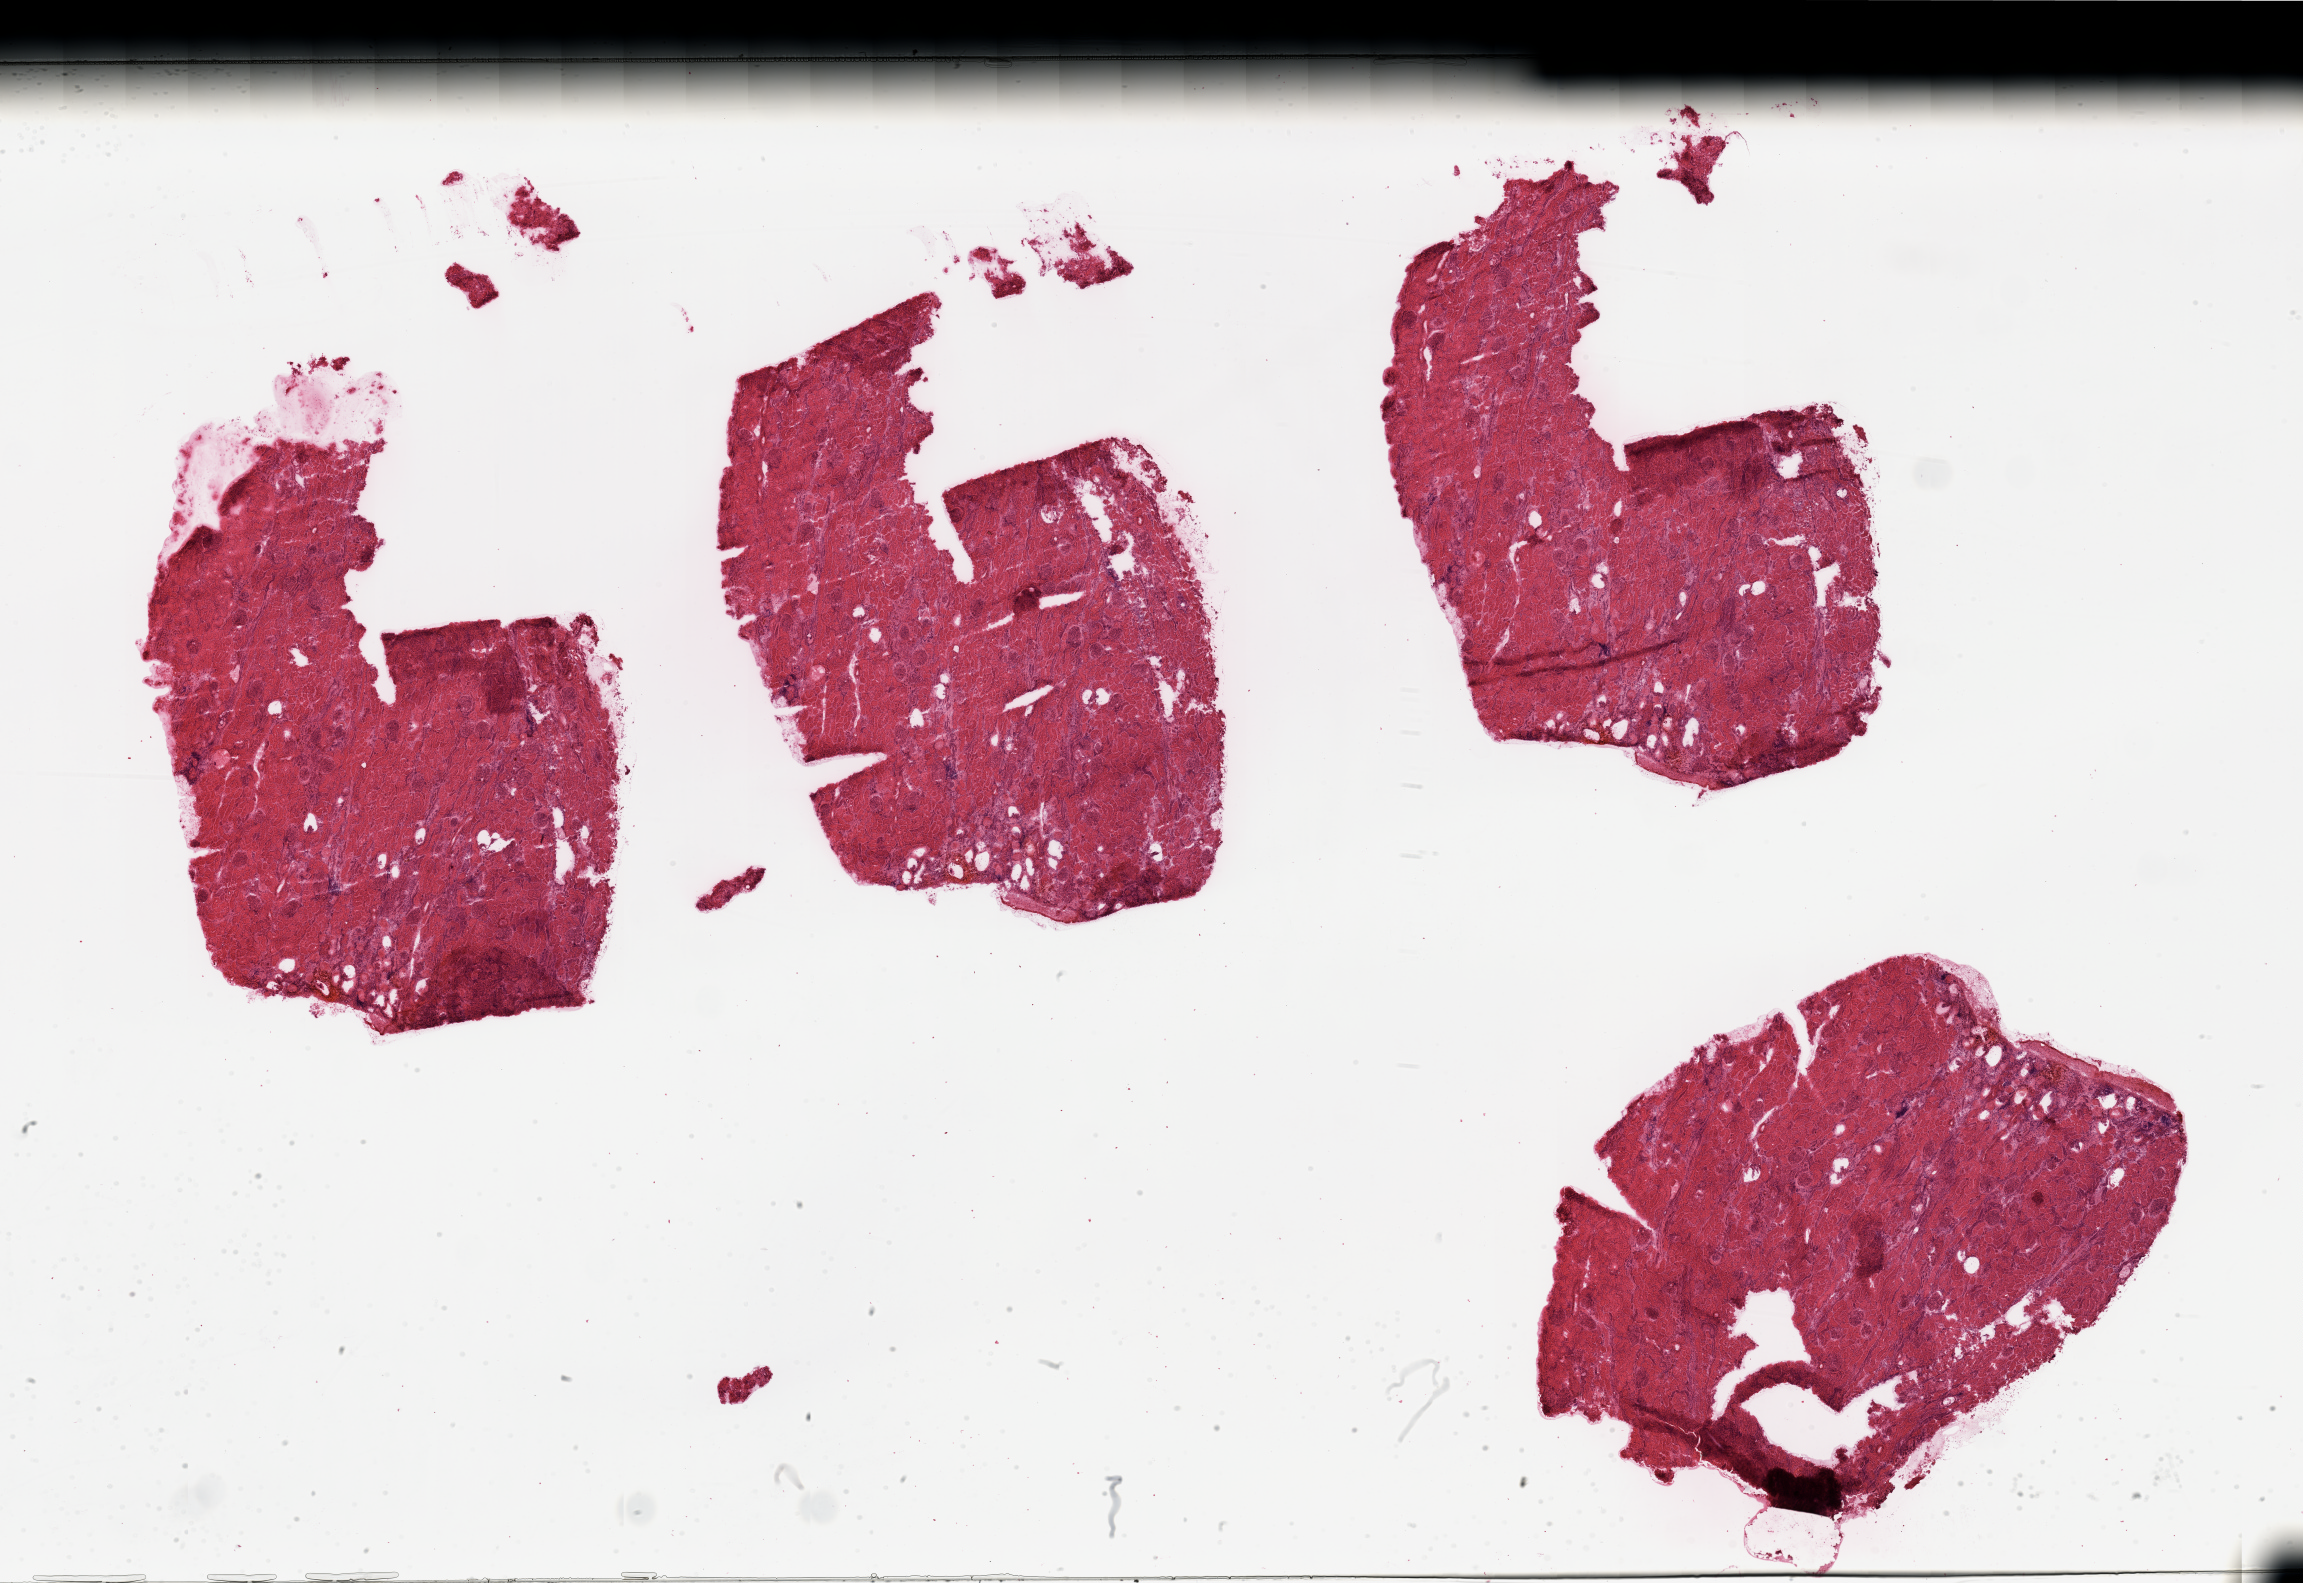
H&E whole-slide image, low-resolution overview of the scanned area, about 36.4 x 25.0 mm. Normal (non-tumour) tissue sample, sampled site: kidney. Patient: female, age 69 years.
This section: normal (non-tumour) tissue from the same patient. Patient diagnosis: Renal cell carcinoma, NOS.